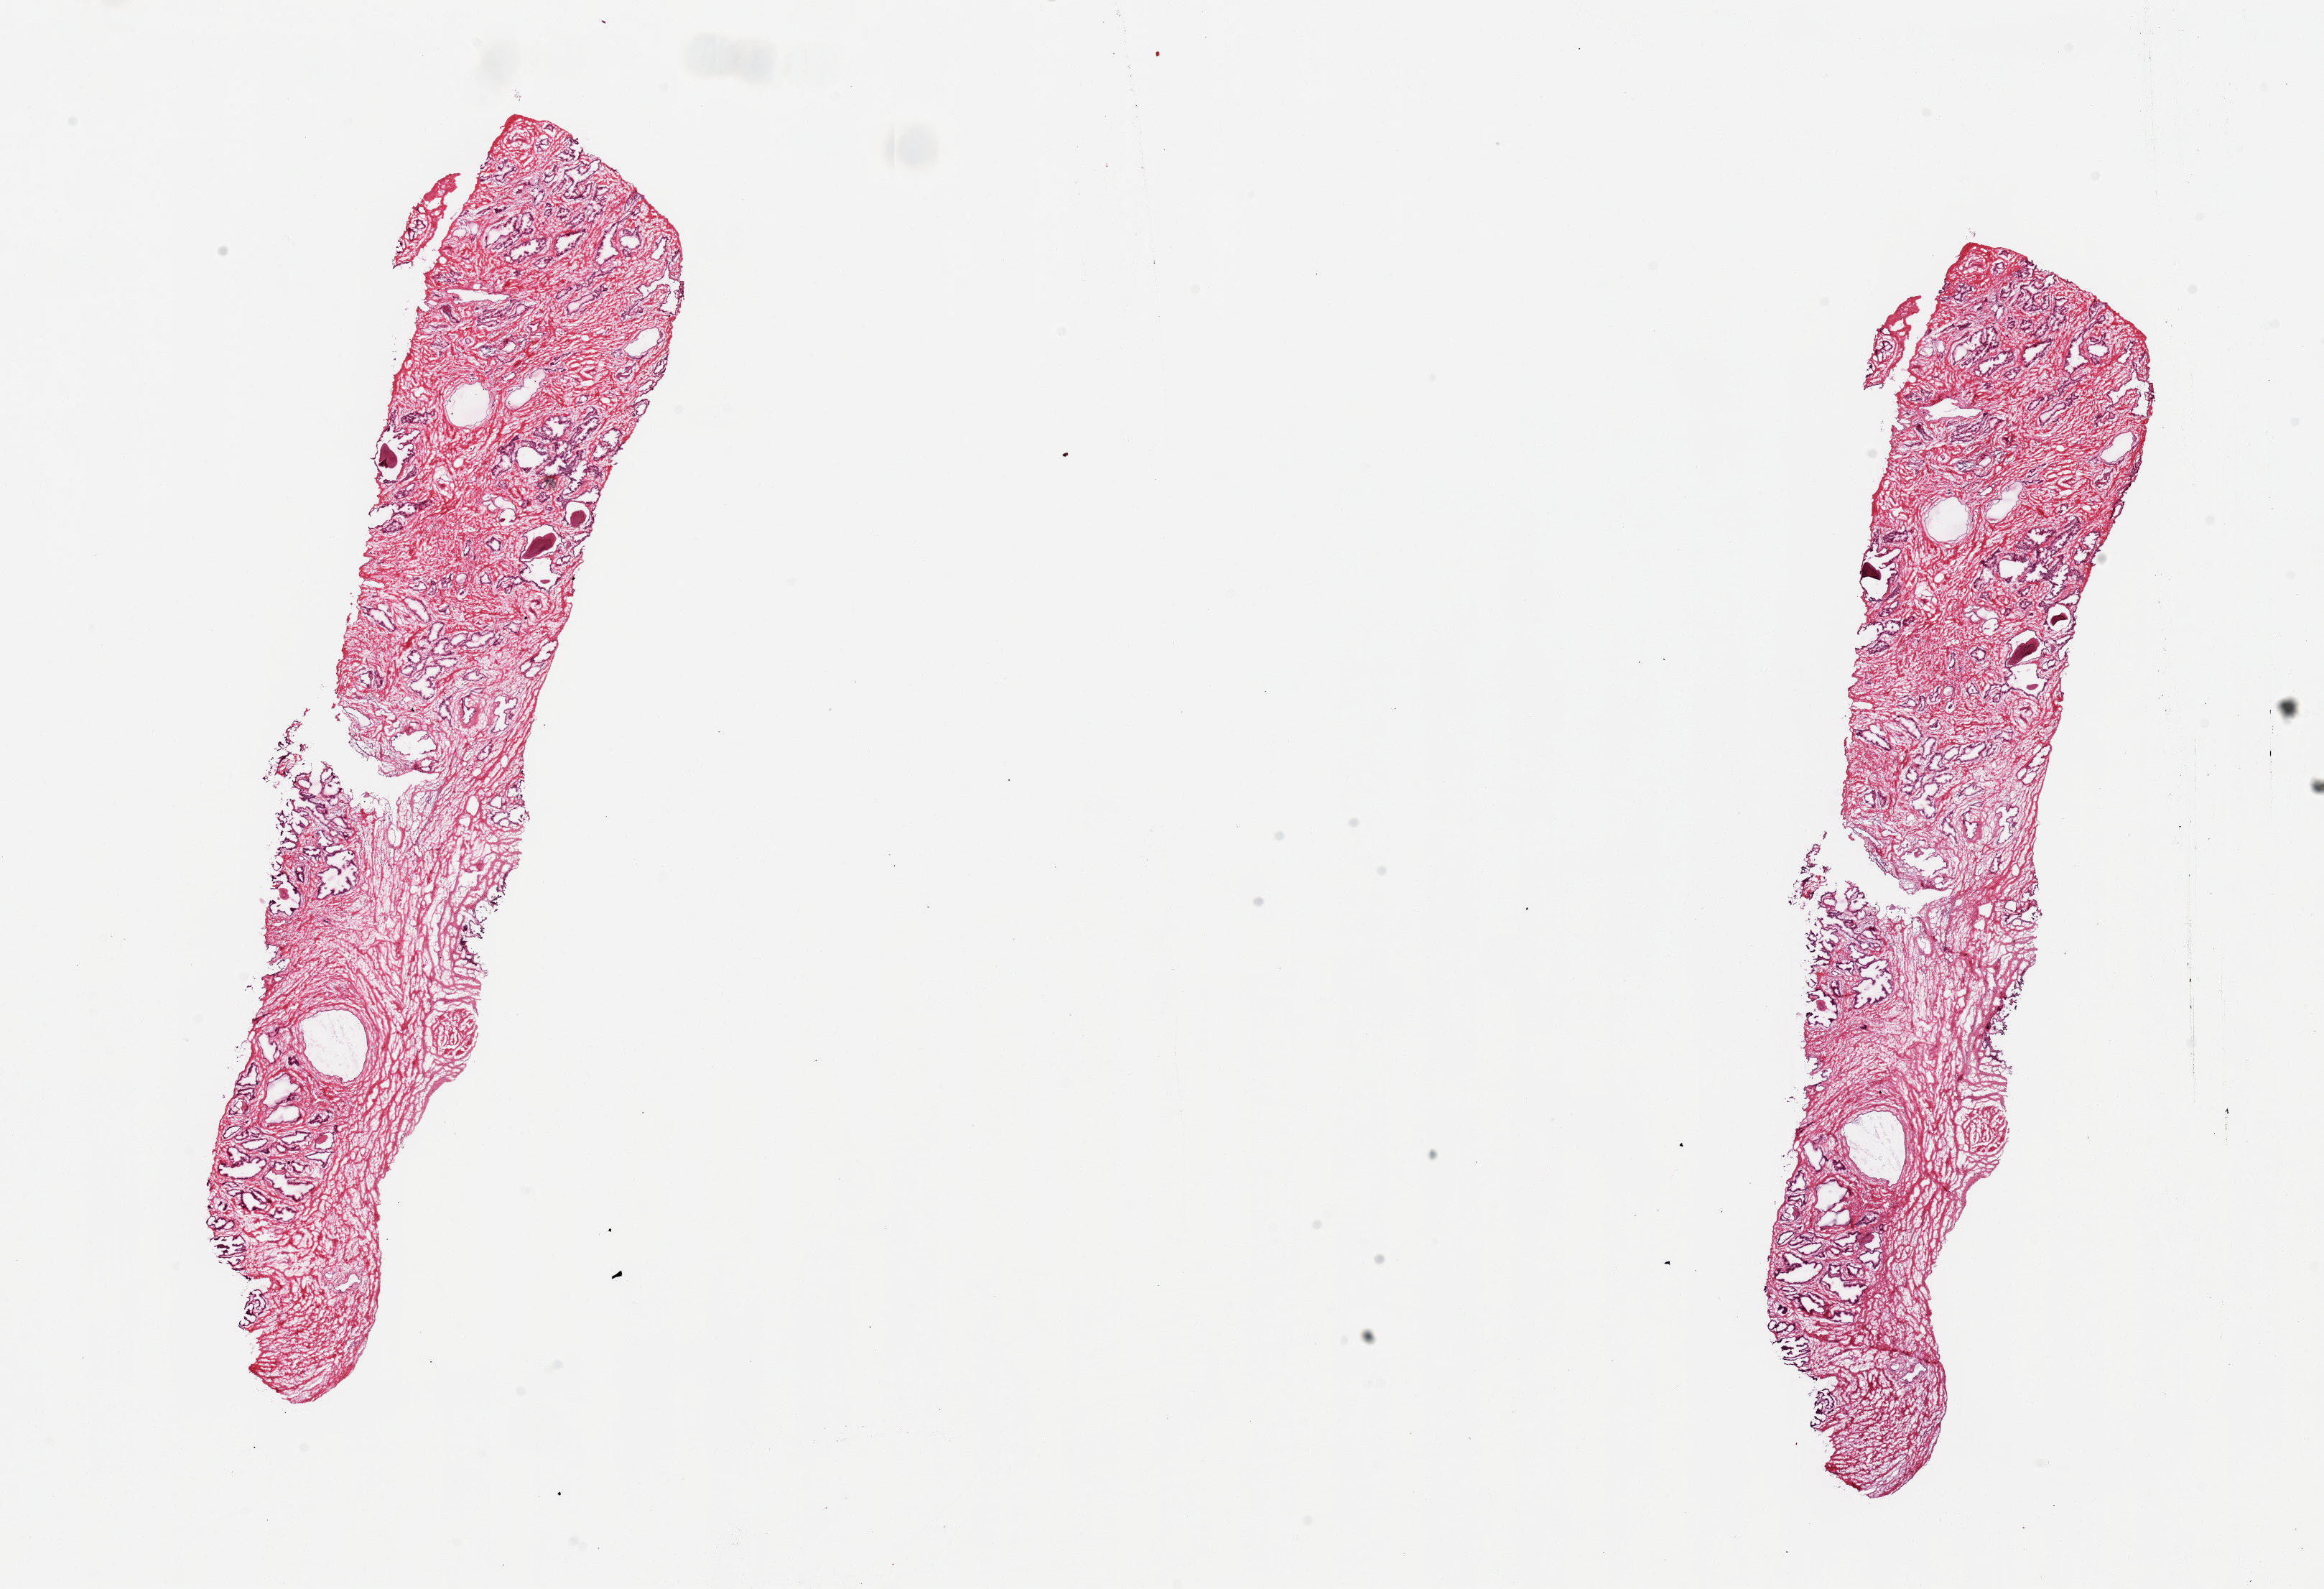
Whole-slide image, H&E stain — low-resolution overview of the scanned area, about 25.6 x 17.5 mm. Frozen section (dry ice). Target tissue: prostate. Donor tissue sample. Donor: male.
Pathologist's review note for this sample: 1 piece (2 sections on slide); more glands than in PAXgene specimen.